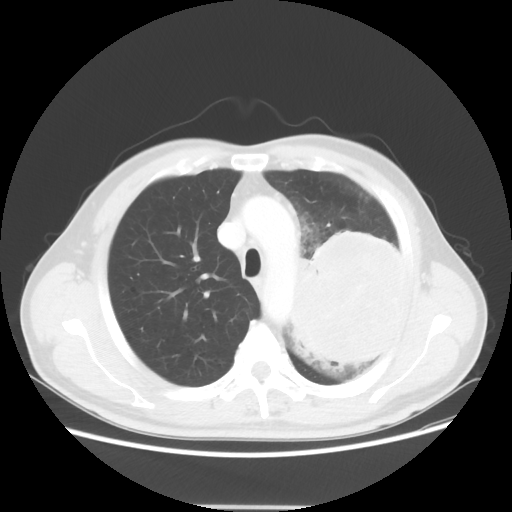
Chest CT, one axial slice; position 40 of 53 along the scan axis; lung window (W 1500 / L -600 HU); 512 × 512 image matrix. Patient: male, 60 years. Case-level facts recorded for this patient, not image findings: clinical TNM (as recorded): T4 N1 M1a.
Annotated regions visible in this slice (bounding box drawn by a radiologist):
- lung tumour (recorded histology: large cell carcinoma): box from (x=279, y=233) to (x=404, y=374) px